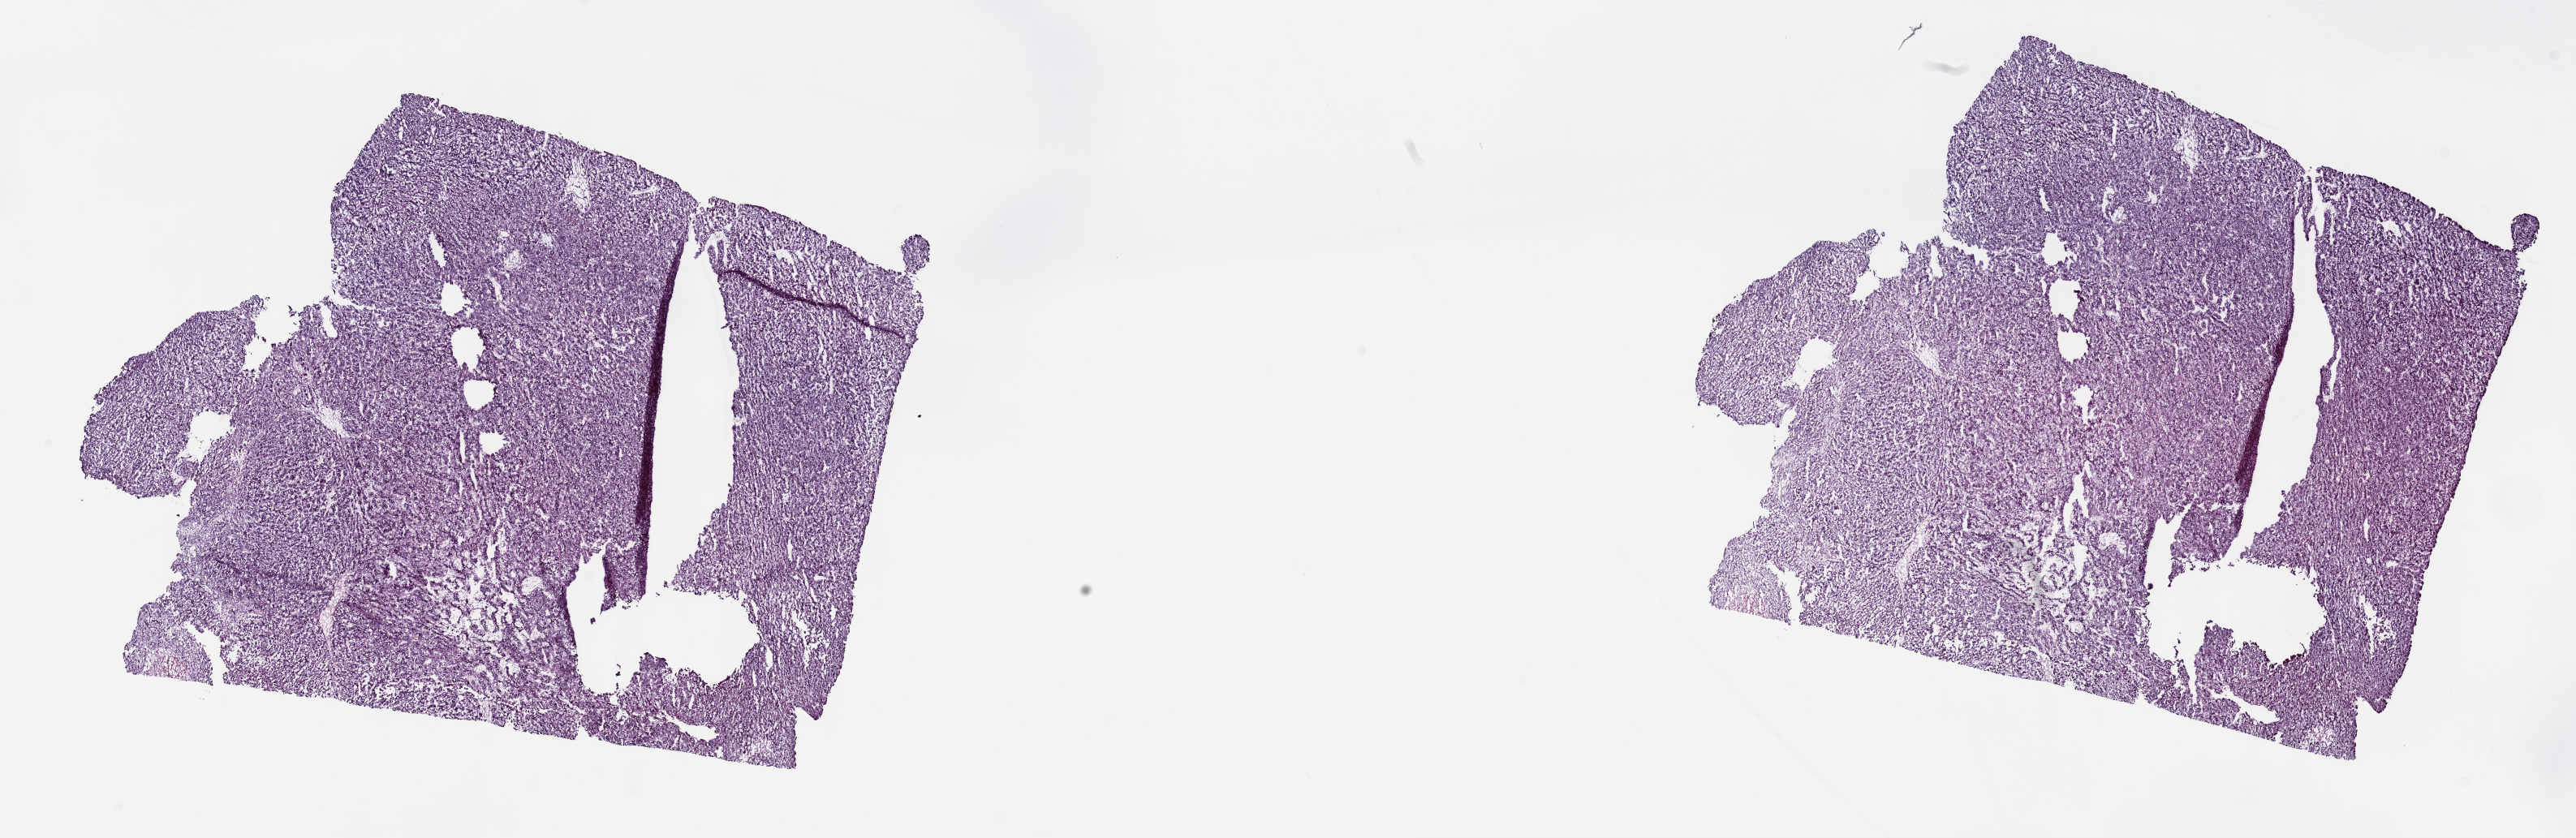
Whole-slide histology image, Hematoxylin and eosin (H&E) stained, low-resolution overview of the scanned area, about 25.7 x 8.4 mm. Frozen section from the top of the tissue portion. Liver, primary tumour sample. Patient: female, age at initial diagnosis 83 years. Histologic grade: G1 (well differentiated). Composition of this section per pathologist review: tumour cells 100%, tumour nuclei 80%, normal cells 0%, stromal cells 0%, necrosis 0%. Inflammatory infiltration, as recorded: lymphocyte infiltration 2%, monocyte infiltration 0%, neutrophil infiltration 0%.
AJCC pathologic stage: I (7th edition). Pathologic diagnosis: Hepatocellular carcinoma, NOS.